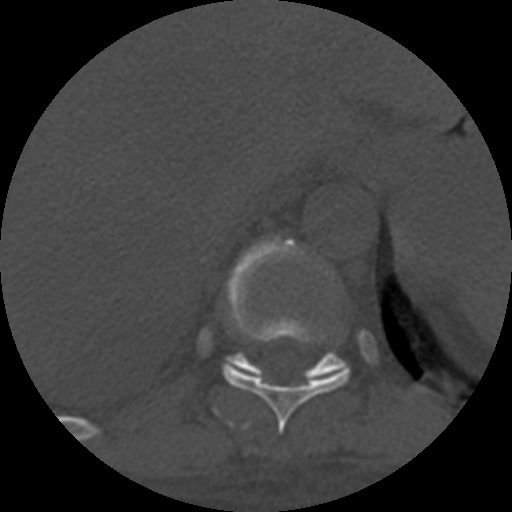
CT including the spine, one axial slice; slice 350 of 708 in the series (ordered by position); one of 3 acquisitions stored at this slice position; bone window (W 1800 / L 400 HU); 1.25 mm slice thickness; 512 × 512 image matrix, field of view 160 × 160 mm. Patient age 55 years. From the clinical record (not read from this slice): primary cancer: colon.
Structures marked on this image (semi-automatic segmentation, software-assisted and operator-edited):
- T10 vertebra: bounding box (x1, y1, x2, y2) in pixels: (221, 235, 351, 433)
- T11 vertebra: (224, 352, 350, 382)